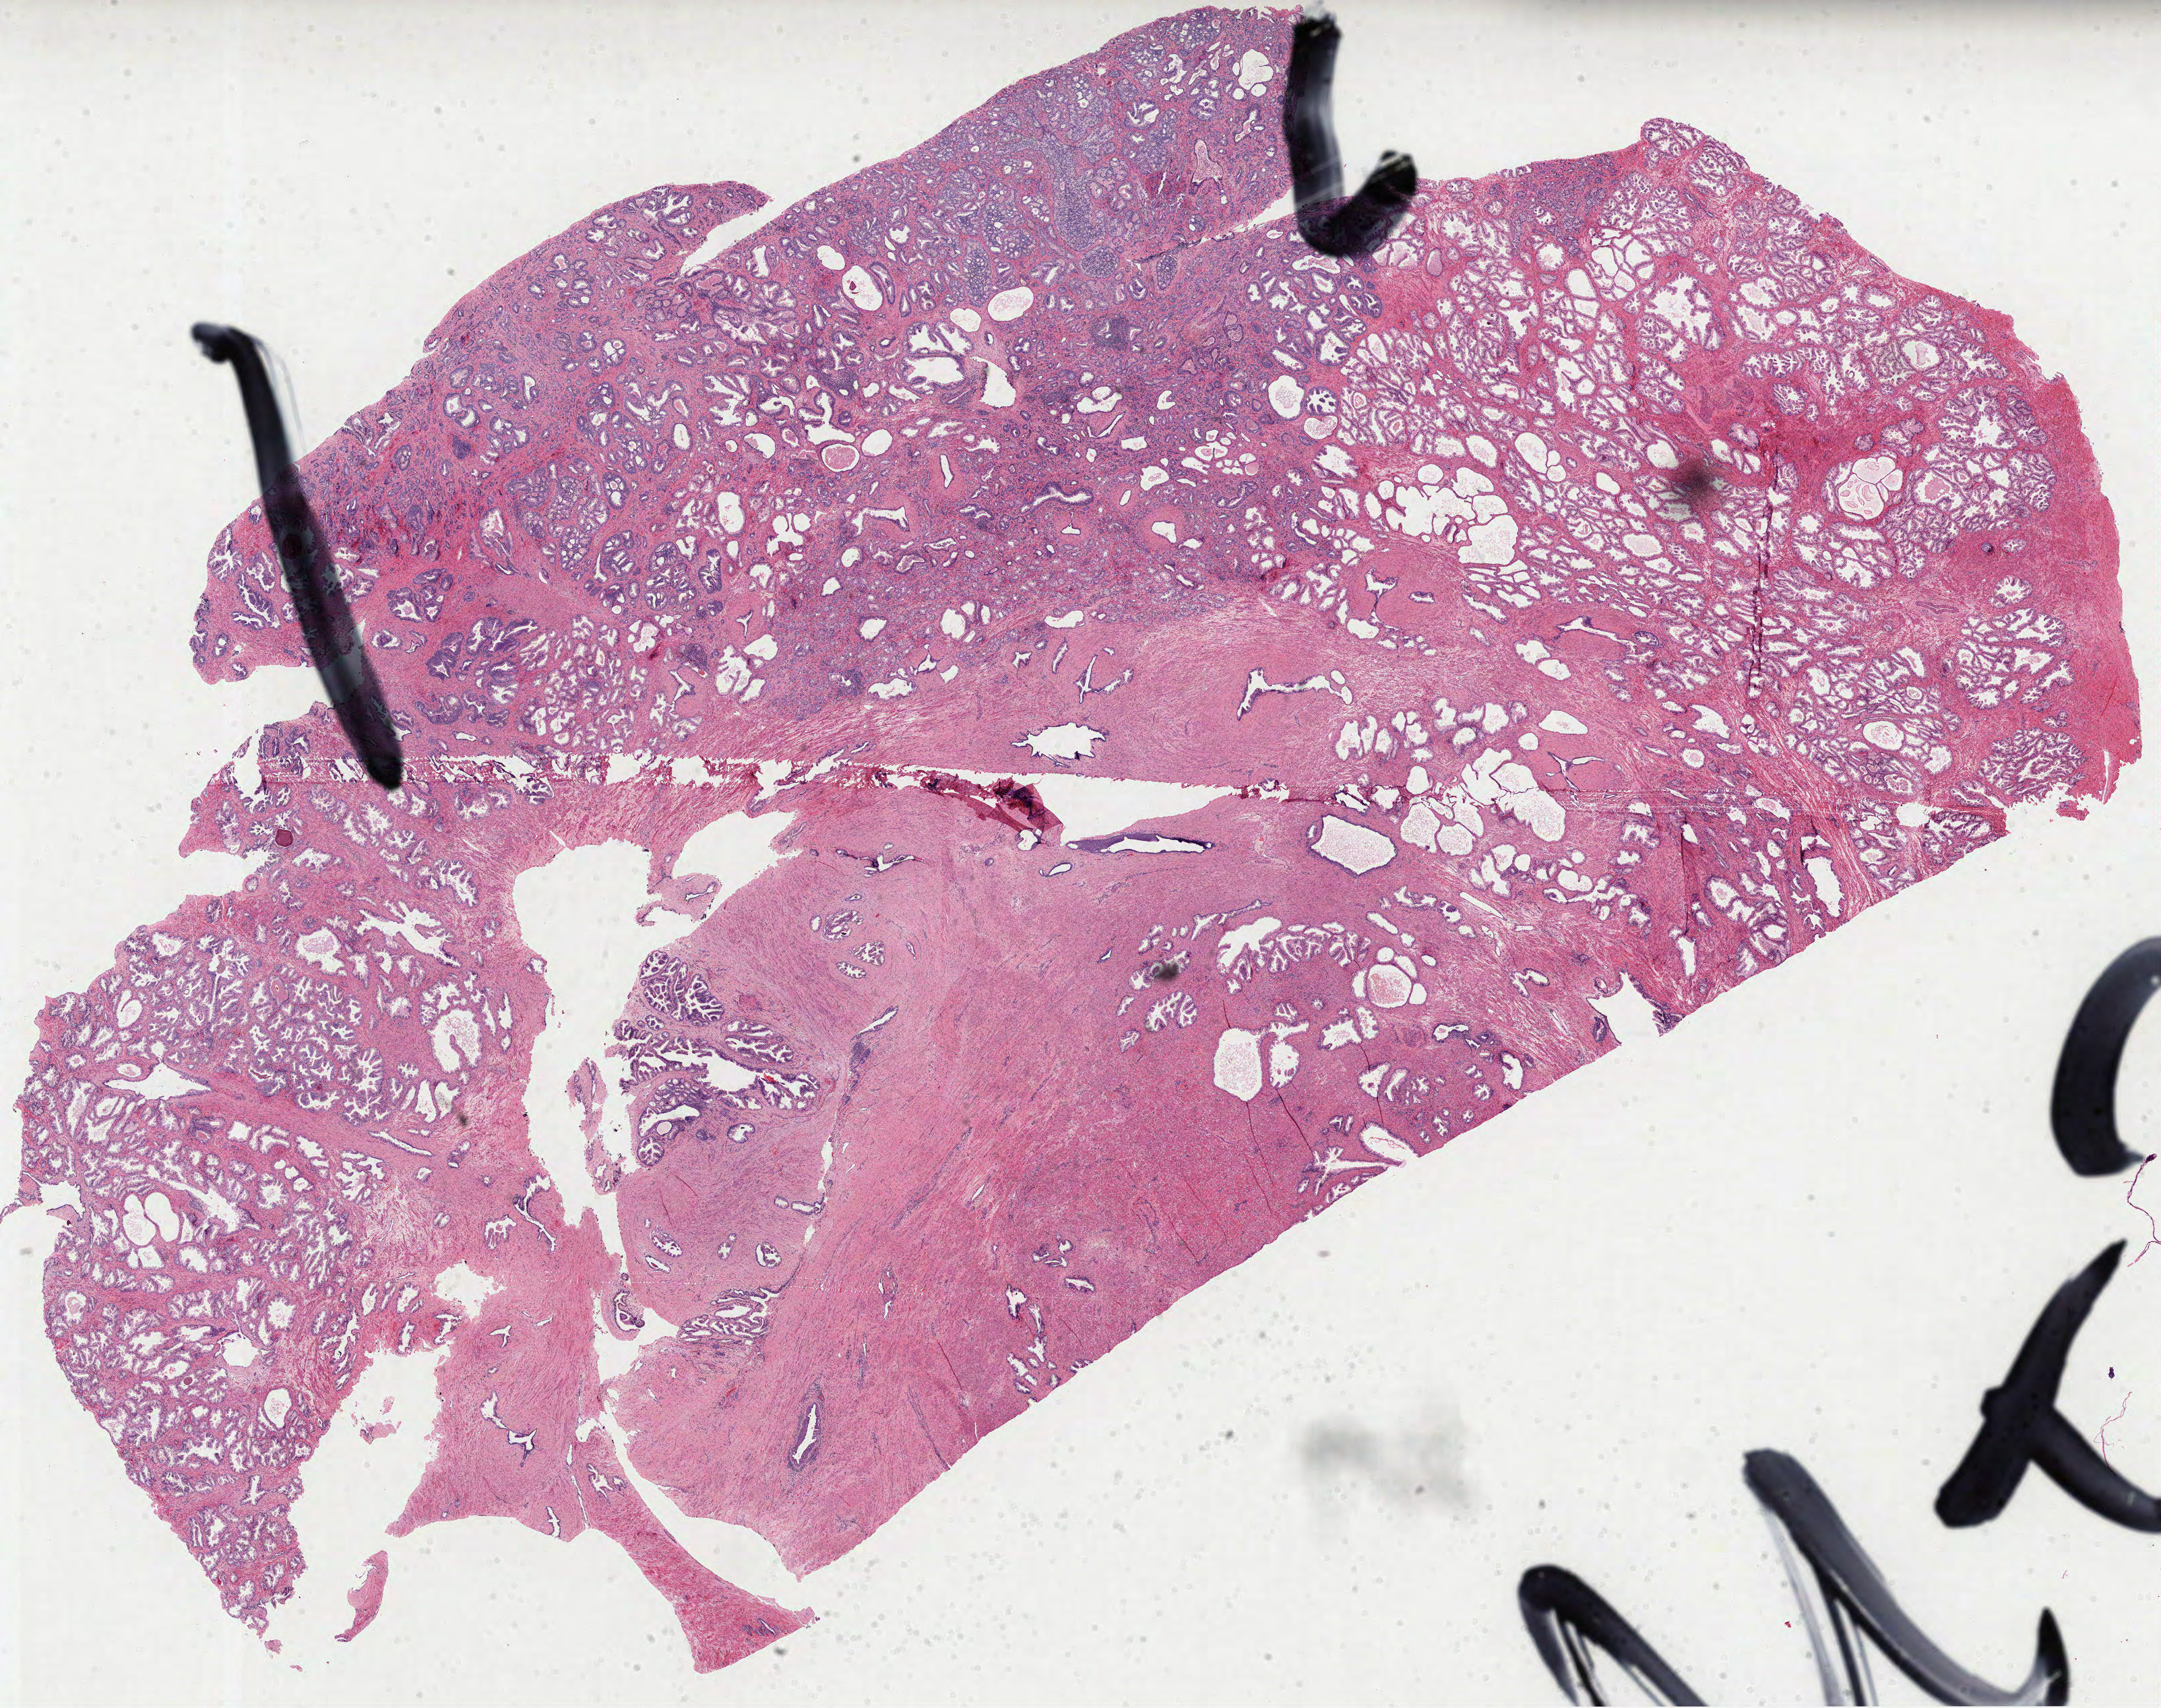
H&E-stained whole-slide image, whole scanned area (about 25.9 x 20.4 mm) shown as a low-resolution overview. FFPE section. Sample: primary tumour, prostate. Male, age 60 years at initial diagnosis. Gleason score: 7 (3+4).
Diagnosis: Acinar cell carcinoma. Laterality: right.